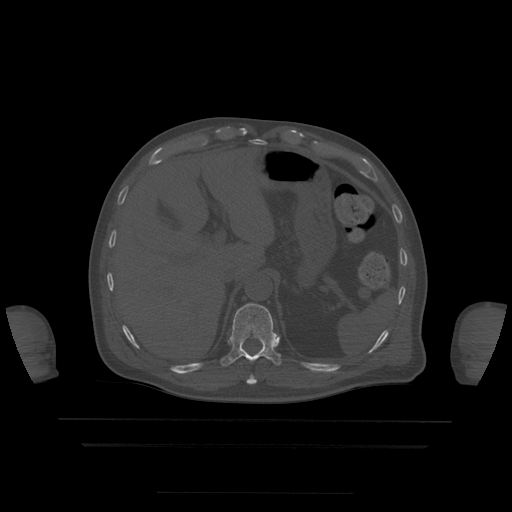
CT including the spine, one axial slice. Slice 222 of 522 in the series (ordered by position). Bone window (W 1800 / L 400 HU). 1.25 mm slice thickness. 512 × 512 image matrix. Patient age 68 years. Case-level facts recorded for this patient, not image findings: primary cancer: urothelial.
Outlined on this slice (semi-automatically segmented with operator editing):
- T10 vertebra: bounding box (x1, y1, x2, y2) in pixels: (247, 375, 257, 385)
- T11 vertebra: (221, 303, 281, 367)